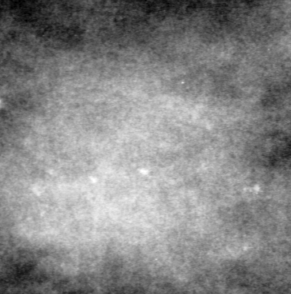
Cropped region of a digitized screen-film mammogram centred on a radiologist-marked abnormality, right breast, CC view, BI-RADS breast density category 3 (scale 1–4).
Mass, shape round, margins ill defined; BI-RADS assessment category 4; subtlety rating 3 on a 1 (subtle) to 5 (obvious) scale; pathology result (as recorded, not read from the image): malignant.